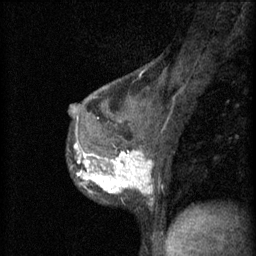
Breast MRI (dynamic contrast-enhanced), one sagittal slice. Position 35 of 60 along the scan axis. 3 images stored at this slice position (order not interpretable as contrast timing). 1.5 T. TE 4.2 ms, TR 11 ms. 256 × 256 image matrix. Female patient, age 37 years.
Structures marked on this image (semi-automatically segmented with operator editing):
- analysis volume of interest (the breast-tissue region the enhancement analysis was run in; not a lesion): bounding box (x1, y1, x2, y2) in pixels: (67, 138, 157, 203)
- tumour enhancement mask (voxels above the 70 % enhancement threshold inside the analysis volume of interest): (75, 142, 153, 195)